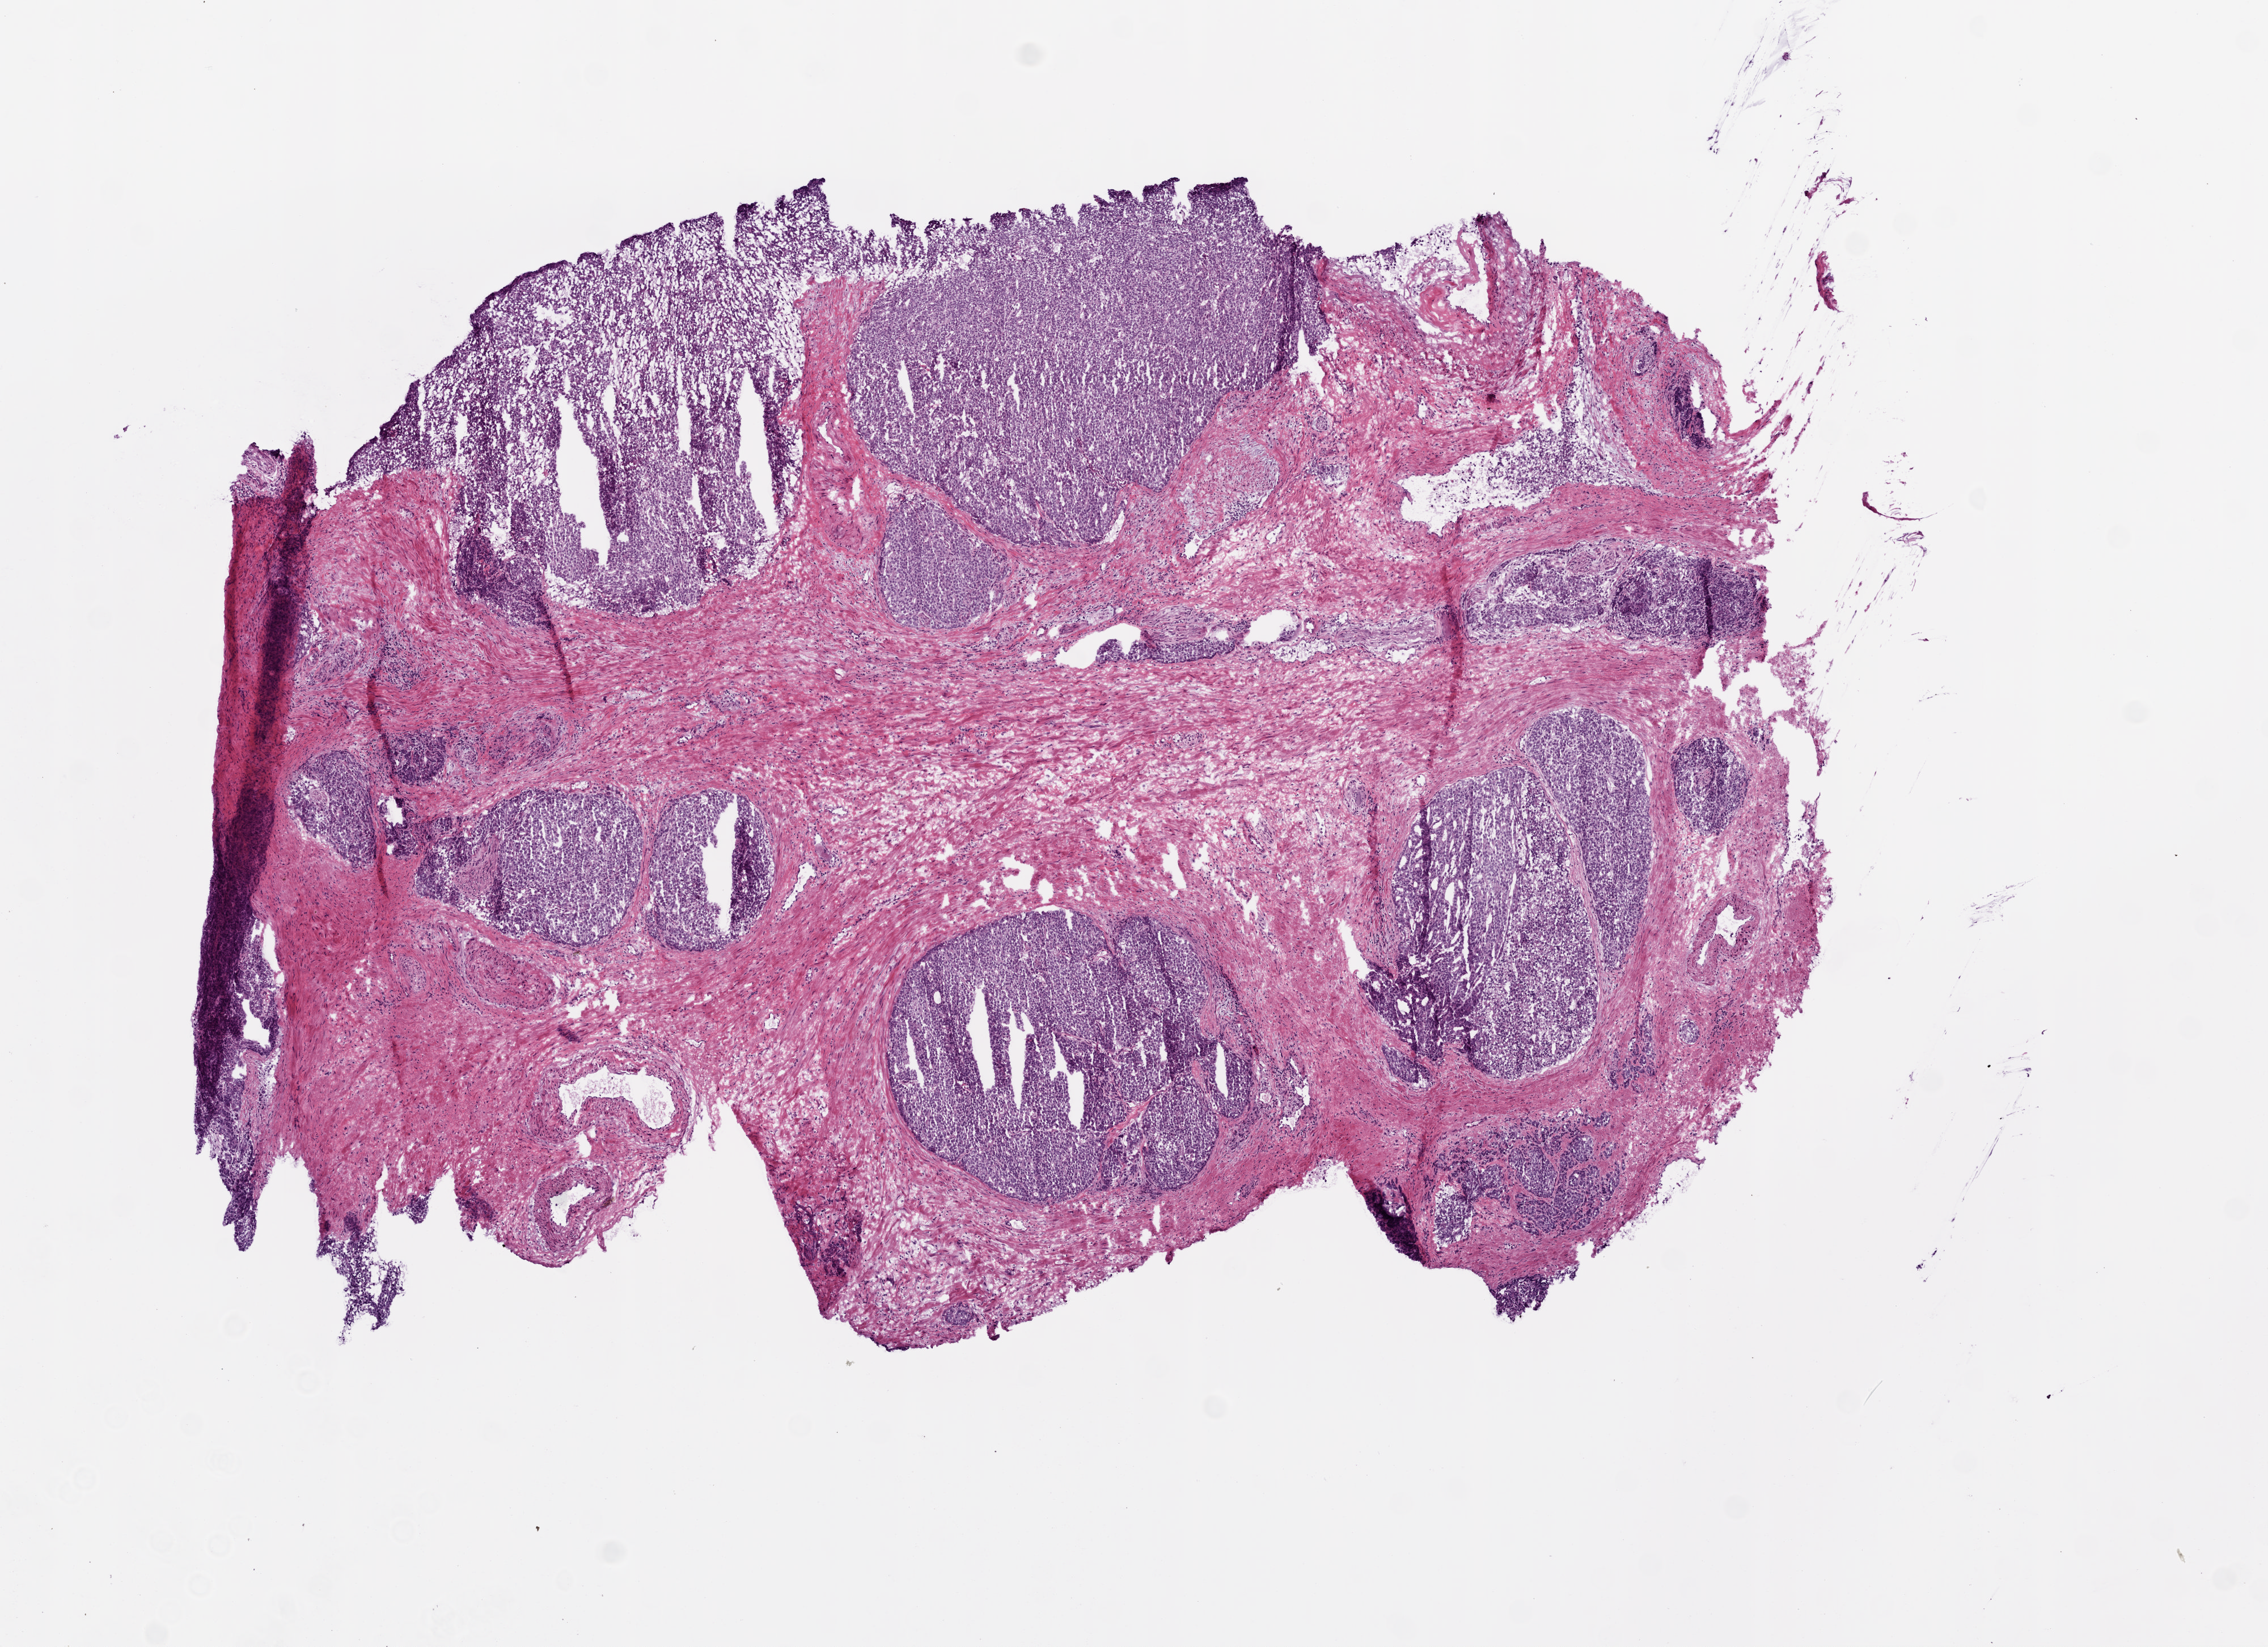
H&E whole-slide image — whole scanned area (about 8.0 x 5.8 mm, acquisition: 20x scan) shown as a low-resolution overview, frozen section from the top of the tissue portion, primary tumour sample from the prostate. Patient: male, age at initial diagnosis 66 years. Gleason score: 8 (4+4). Pathologist review of this section (percent, as recorded): tumour cells 50%, tumour nuclei 65%, normal cells 0%, stromal cells 45%, necrosis 5%. Infiltration values recorded for this section: lymphocyte infiltration 2%, monocyte infiltration 0%, neutrophil infiltration 0%.
* lymph nodes positive (case pathology): 0 of 9 examined
* laterality: bilateral
* histologic diagnosis: Acinar cell carcinoma (prostate gland)